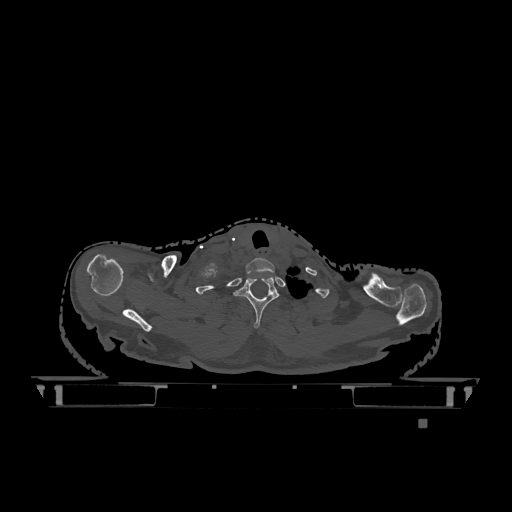
CT including the spine, one axial slice. Position 999 of 1317 along the scan axis. Bone window (W 1800 / L 400 HU). 0.5 mm slice thickness. 512 × 512 image matrix, field of view 500 × 500 mm. Female patient, age 74 years. From the clinical record (not read from this slice): primary cancer: lung; vertebrae with lytic lesions (as recorded): T1, T4, T5, T6, L4, L5.
Outlined on this slice (semi-automatically segmented with operator editing):
- T1 vertebra: bounding box (x1, y1, x2, y2) in pixels: (234, 276, 279, 328)